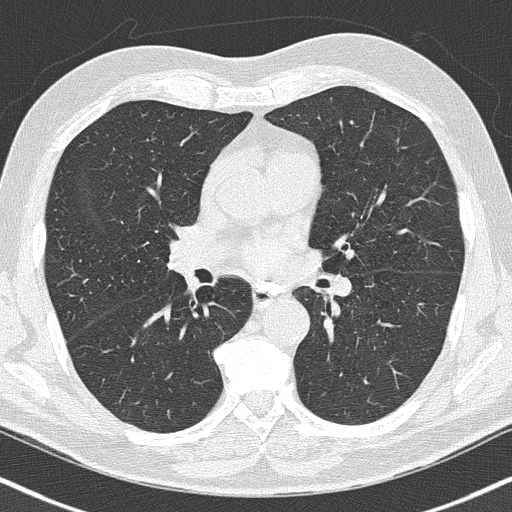
Chest CT (low-dose screening protocol), one axial image, first (baseline) screen, lung window (W 1500 / L -600 HU), 2 mm slice thickness, 120 kVp, slice 86 of 186 in the series. Male participant, aged 66 years at enrolment.
Expert-annotated lung lesion, box from (x=184, y=269) to (x=210, y=298) px. Reader record for this screening exam (exam-level; its link to the box is not recorded): non-calcified nodule or mass ≥4 mm, right upper lobe, 5 × 4 mm, smooth margins. Participant outcome: lung cancer diagnosed 778 days after this screen (after the third annual screen) — squamous cell carcinoma, NOS, right lower lobe, poorly differentiated (G3), stage IIA (AJCC 6th edition), 22 mm at pathology.